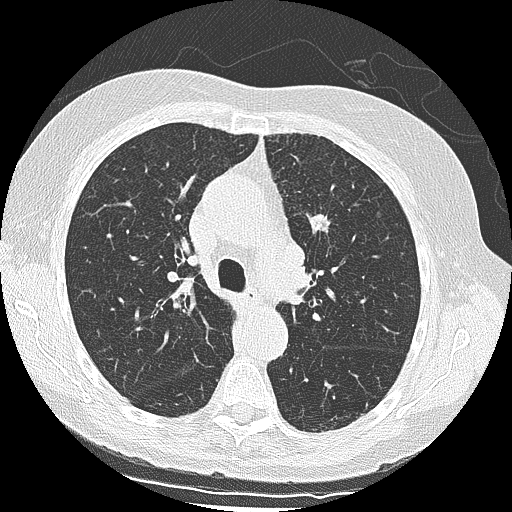
Low-dose screening chest CT, one axial slice. Position 96 of 139 along the scan axis. Reconstruction kernel LUNG. Lung window (W 1500 / L -600 HU). 2.5 mm slice thickness. 512 × 512 image matrix, field of view 318 × 318 mm.
Outlined on this slice (expert manual segmentation):
- lesion 1 (tumor, upper lobe of left lung): bounding box <306,213,331,239> (left, top, right, bottom; pixels)